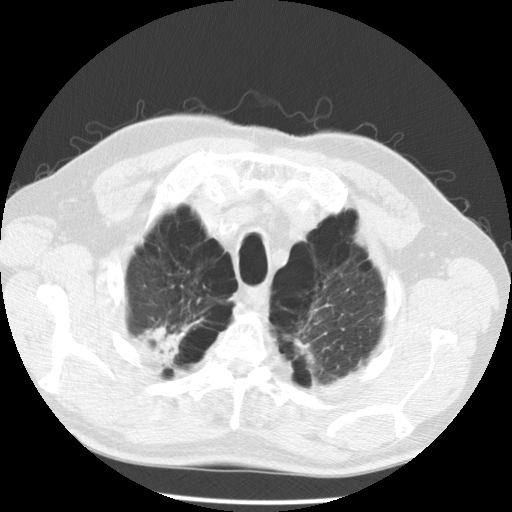
Chest CT (low-dose screening protocol), one axial image; second annual screen; lung window (W 1500 / L -600 HU); 2.5 mm slice thickness; slice 24 of 167 in the series. Male participant, aged 68 years at enrolment. Former smoker at enrolment.
Expert-annotated lung lesion, bounding box (x1, y1, x2, y2) in pixels: (127, 300, 201, 373). The screening reader recorded 2 non-calcified nodules or masses ≥4 mm on this exam (lingula, left lower lobe); which of them this box marks is not recorded. Official screen result: positive, no significant change: stable abnormalities potentially related to lung cancer, unchanged since the prior screening exam. Later outcome: lung cancer diagnosed 617 days after this screen — large cell carcinoma, NOS, right upper lobe, poorly differentiated (G3), stage IV (AJCC 6th edition).